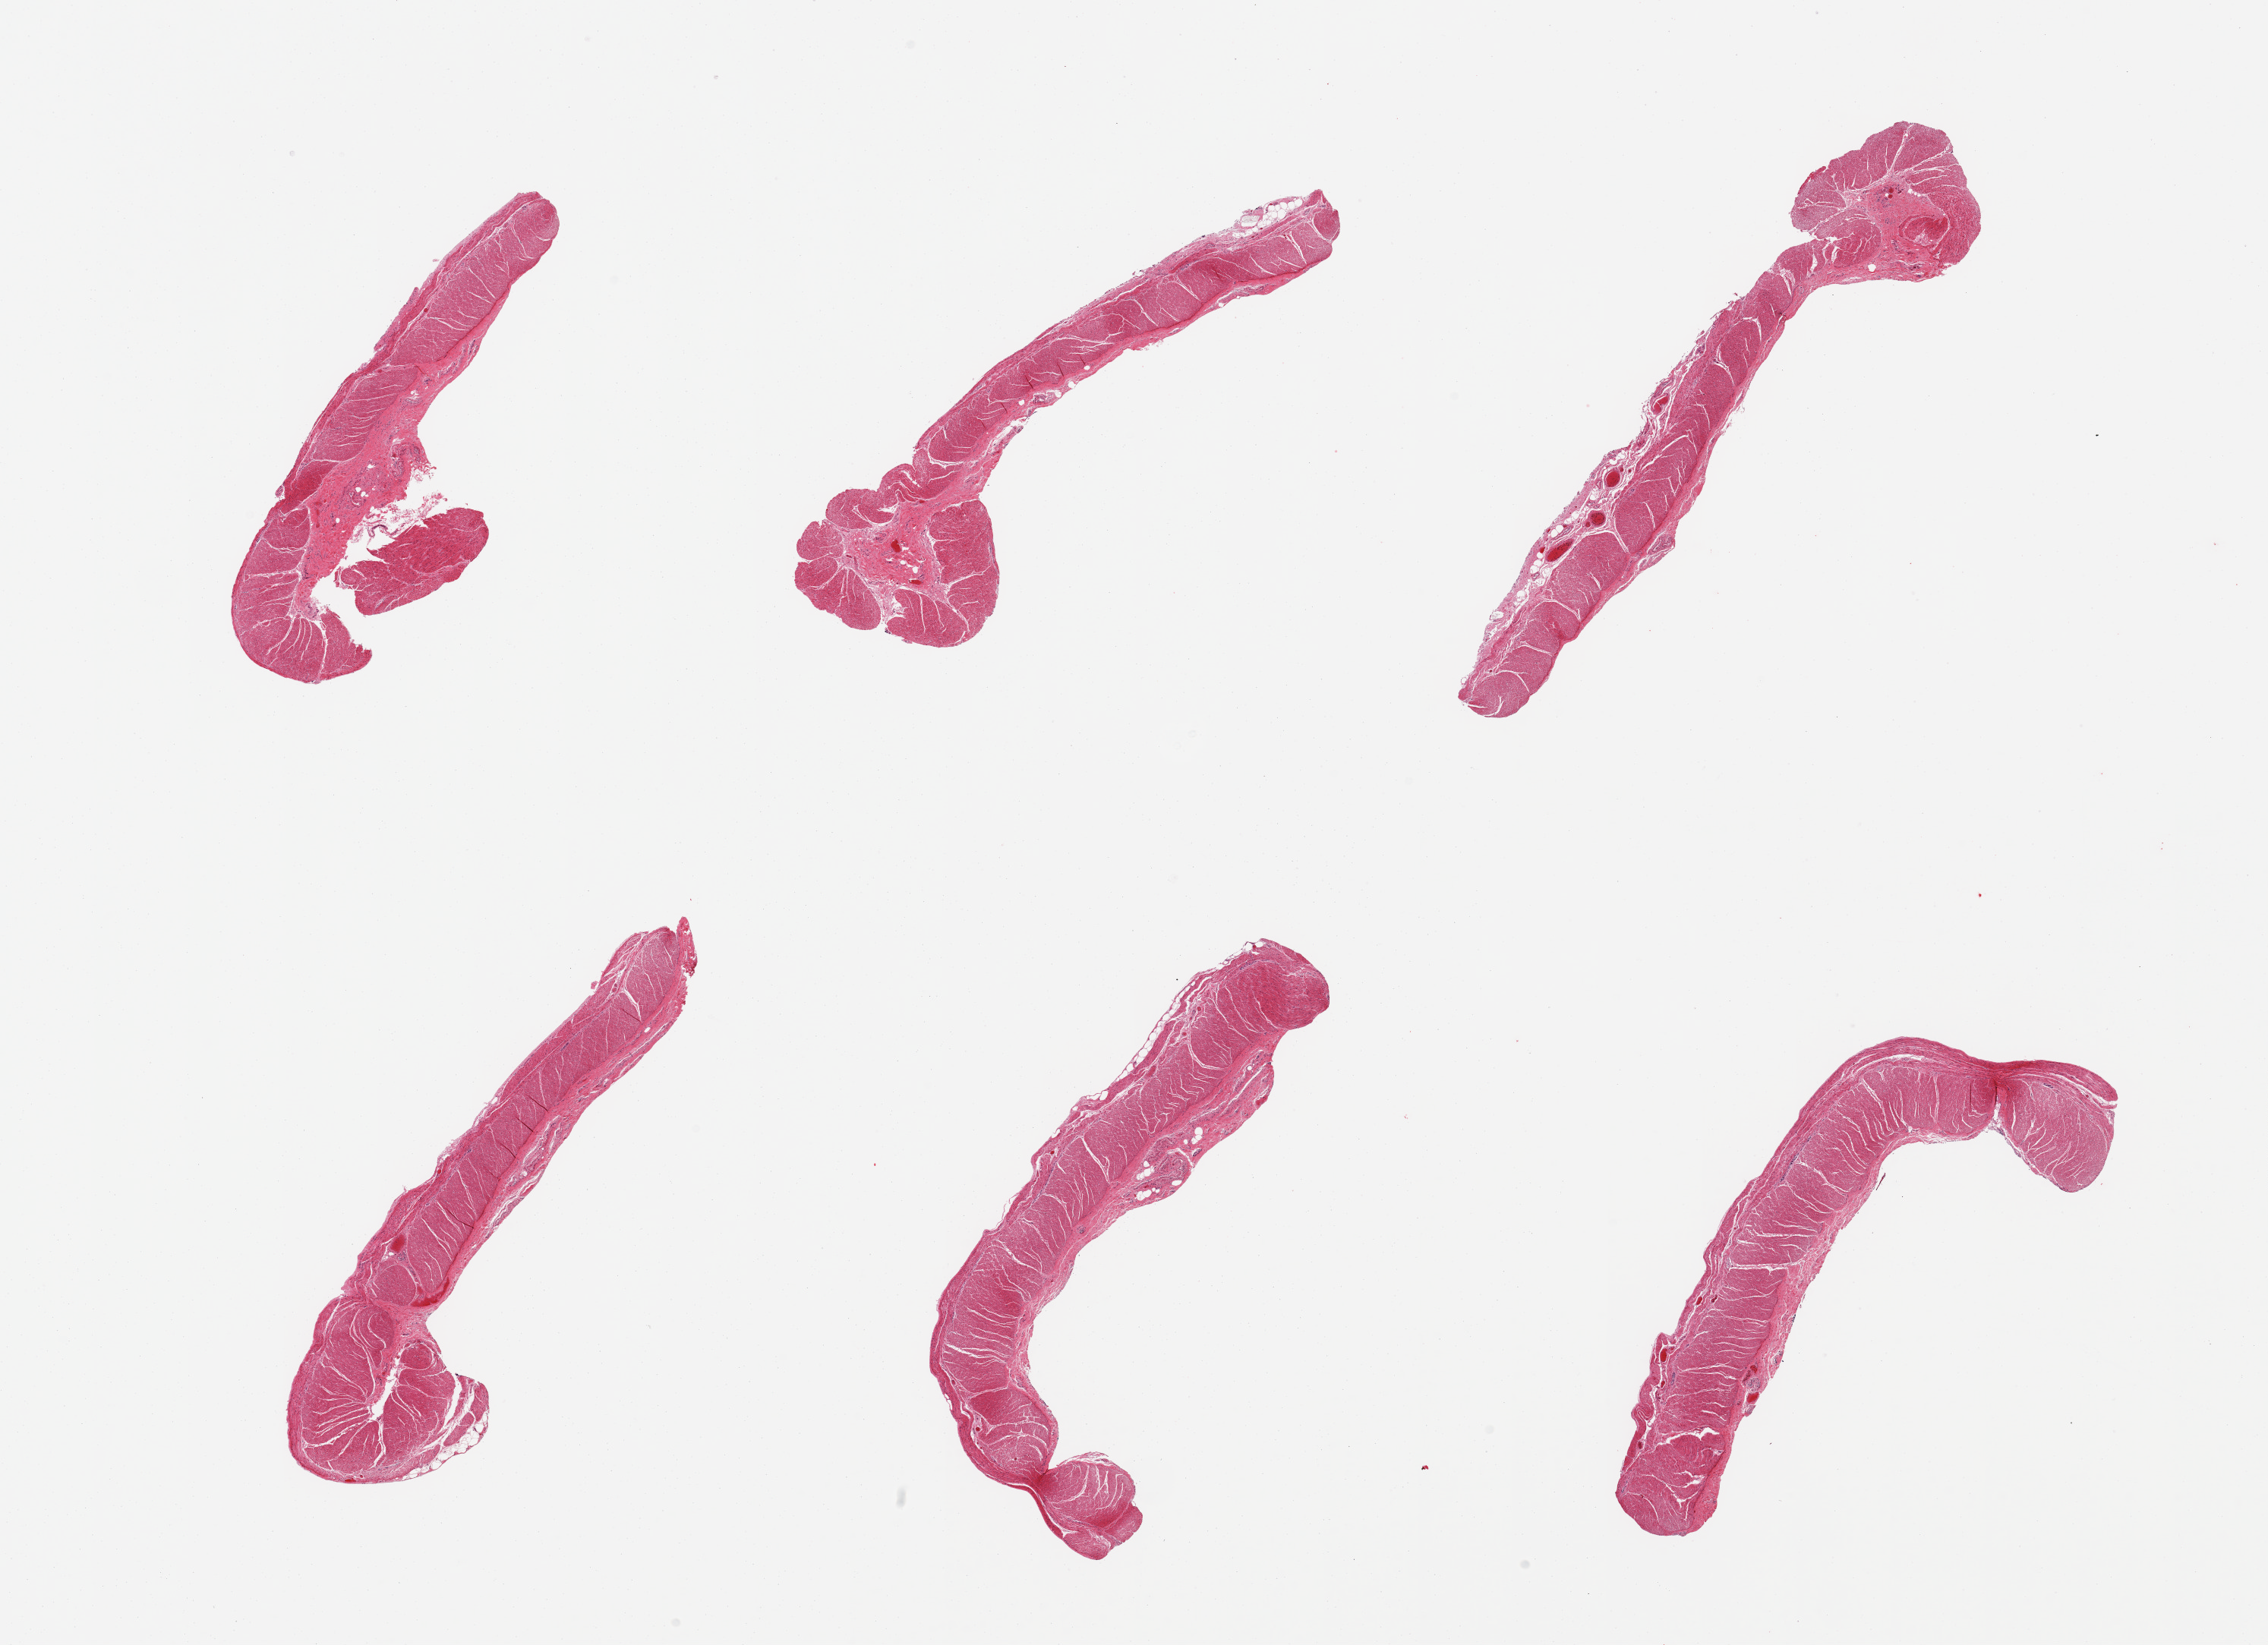
Haematoxylin and eosin whole-slide image — low-resolution overview of the scanned area, about 23.6 x 17.1 mm (from a 20x scan); PAXgene-fixed, paraffin-embedded tissue; sampled site (target tissue): sigmoid colon; tissue donor sample. Donor sex: male.
• review note (as recorded): 6 pieces, confirmed target muscularis